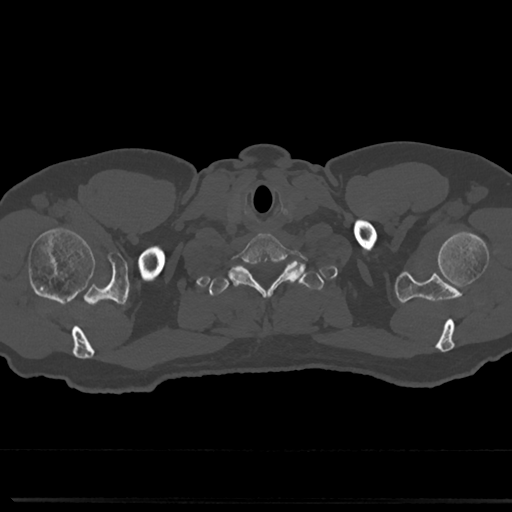
CT including the spine, one axial slice; reconstruction kernel Br40s/3; bone window (W 1800 / L 400 HU); 0.5 mm slice thickness; 512 × 512 image matrix, field of view 355 × 355 mm. Male patient, age 61 years. From the clinical record (not read from this slice): primary cancer: prostate.
Outlined on this slice (semi-automatically segmented with operator editing):
- T1 vertebra: box from (x=209, y=262) to (x=319, y=342) px